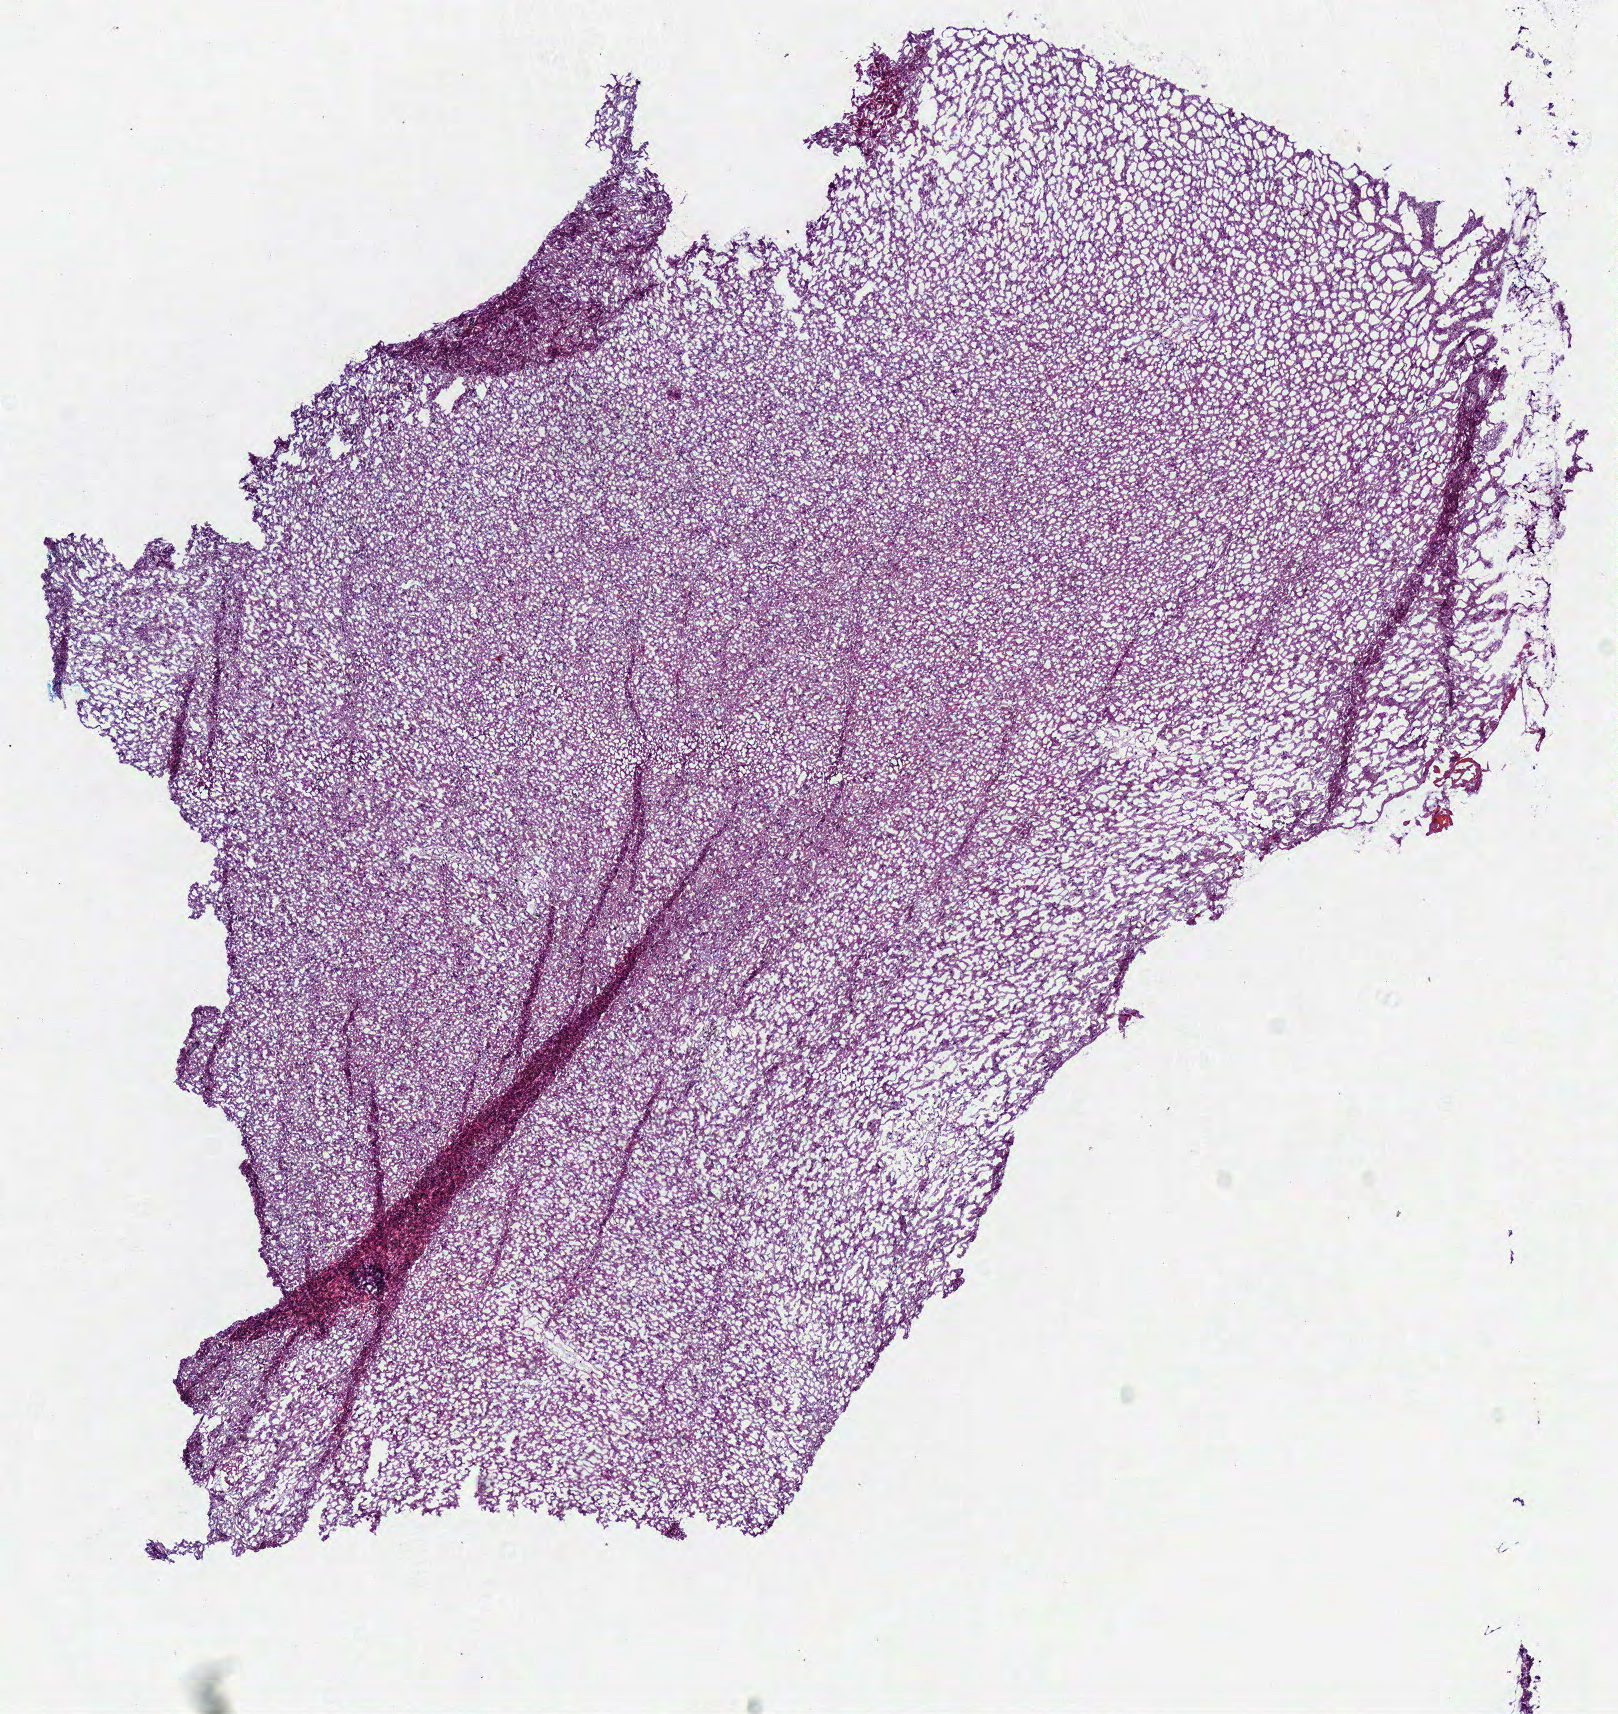
Digitized H&E-stained tissue section (whole slide) — a low-resolution overview of the entire scanned area, about 6.4 x 6.7 mm (acquisition: 40x scan), frozen section, sample: primary tumour, brain. Male patient; age at initial diagnosis 58 years. Pathologist review of this section (percent, as recorded): tumour cells 100%, tumour nuclei 60%.
Histologic diagnosis: Glioblastoma.